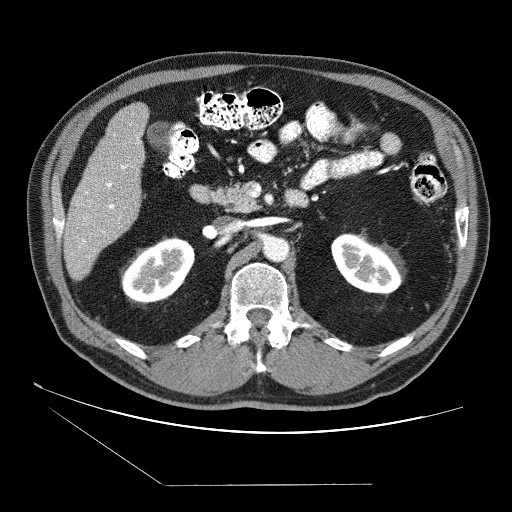
Contrast-enhanced abdominal CT (liver protocol), one axial slice. Slice 24 of 87 in the series (ordered by position). Reconstruction kernel STANDARD. Soft-tissue window (W 400 / L 40 HU). 2.5 mm slice thickness. 512 × 512 image matrix. From the clinical record (not read from this slice): diagnosis: hepatocellular carcinoma (patient treated with transarterial chemoembolisation; whether this scan precedes or follows treatment is not stated here); TNM stage (as recorded): Stage-II; Child-Pugh class: B.
Structures marked on this image (semi-automatic segmentation, software-assisted and operator-edited):
- liver parenchyma outside the tumour (the mass and vessels are separate outlines, so this box may not span the whole liver): bounding box [x1, y1, x2, y2] px = [64, 102, 148, 280]
- liver vessels: [71, 134, 139, 258]